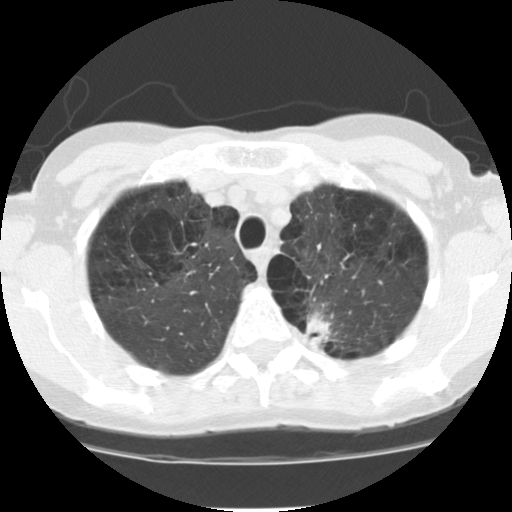
Low-dose screening chest CT, one axial slice. Position 94 of 116 along the scan axis. Reconstruction kernel STANDARD. Lung window (W 1500 / L -600 HU). 512 × 512 image matrix.
Outlined on this slice (manually delineated by an expert):
- lesion 1 (tumor, upper lobe of left lung): bounding box (x1, y1, x2, y2) in pixels: (305, 311, 331, 346)